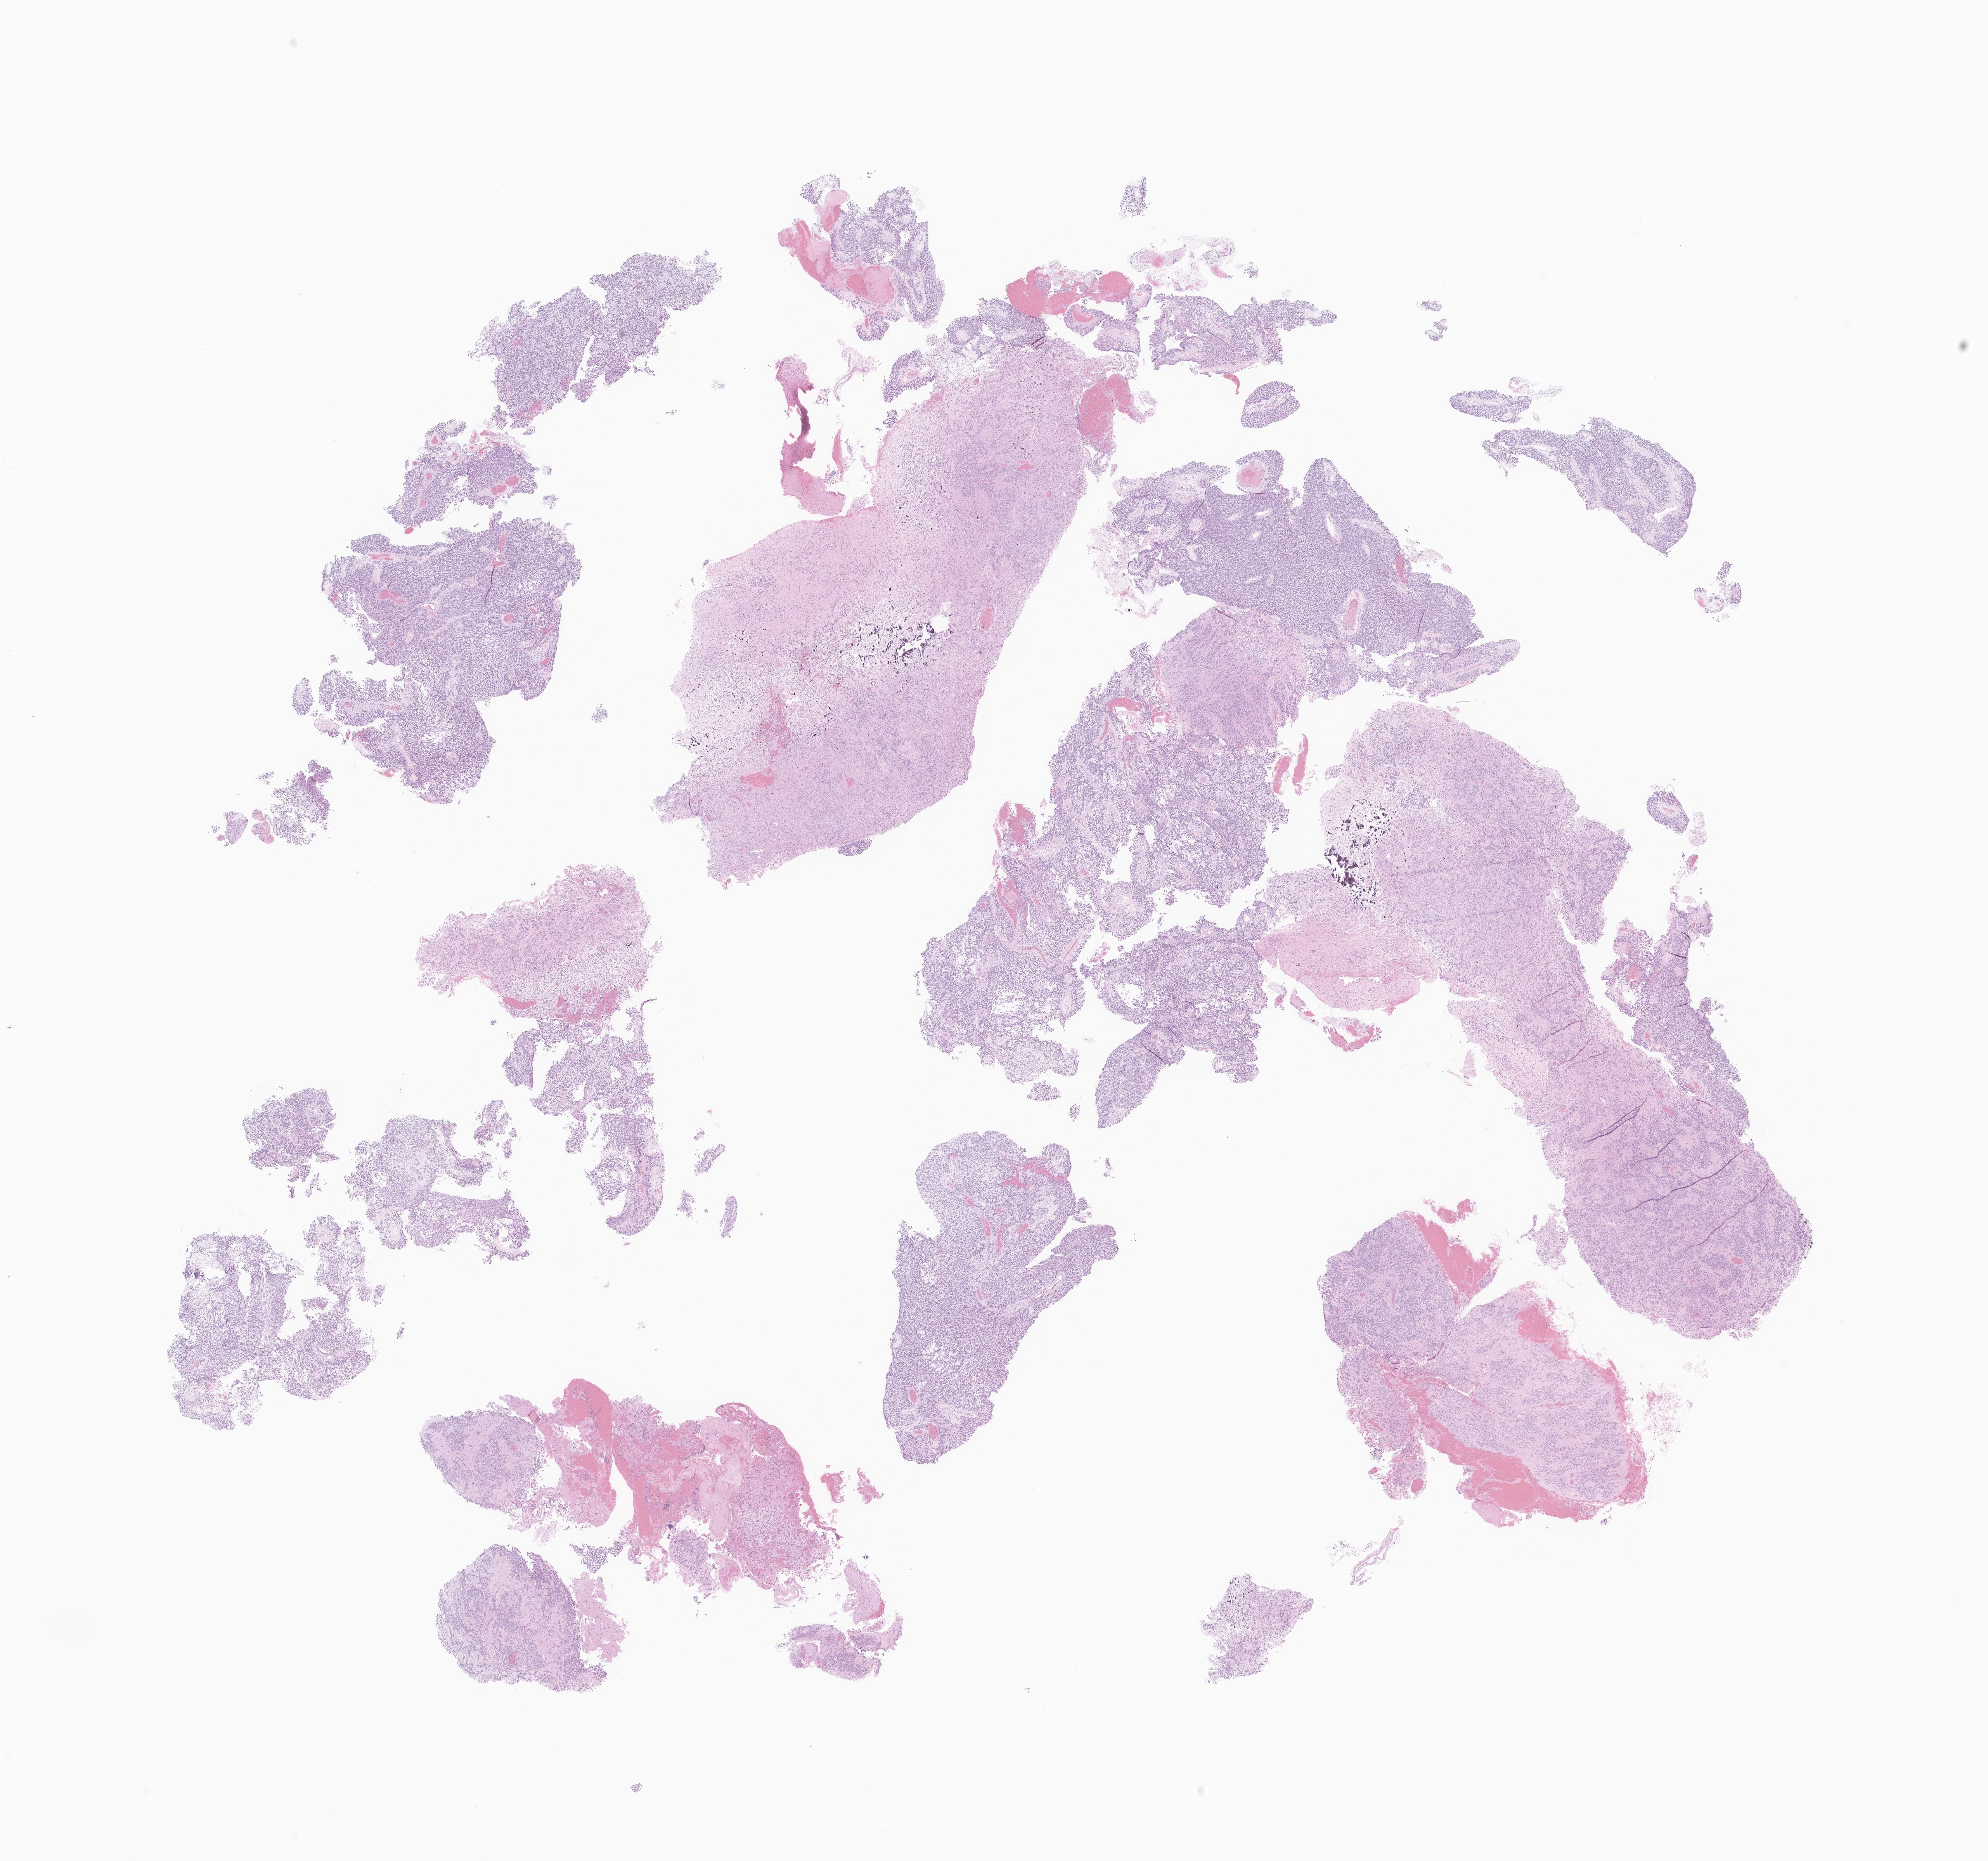
Digitized hematoxylin and eosin (H&E)-stained section of tumor tissue from the occipital lobe, whole scanned area (about 21.6 x 20.2 mm) shown as a low-resolution overview; formalin-fixed, paraffin-embedded (FFPE) tissue. Patient female; age 157 months.
Recorded diagnosis: Ependymoma, NOS.